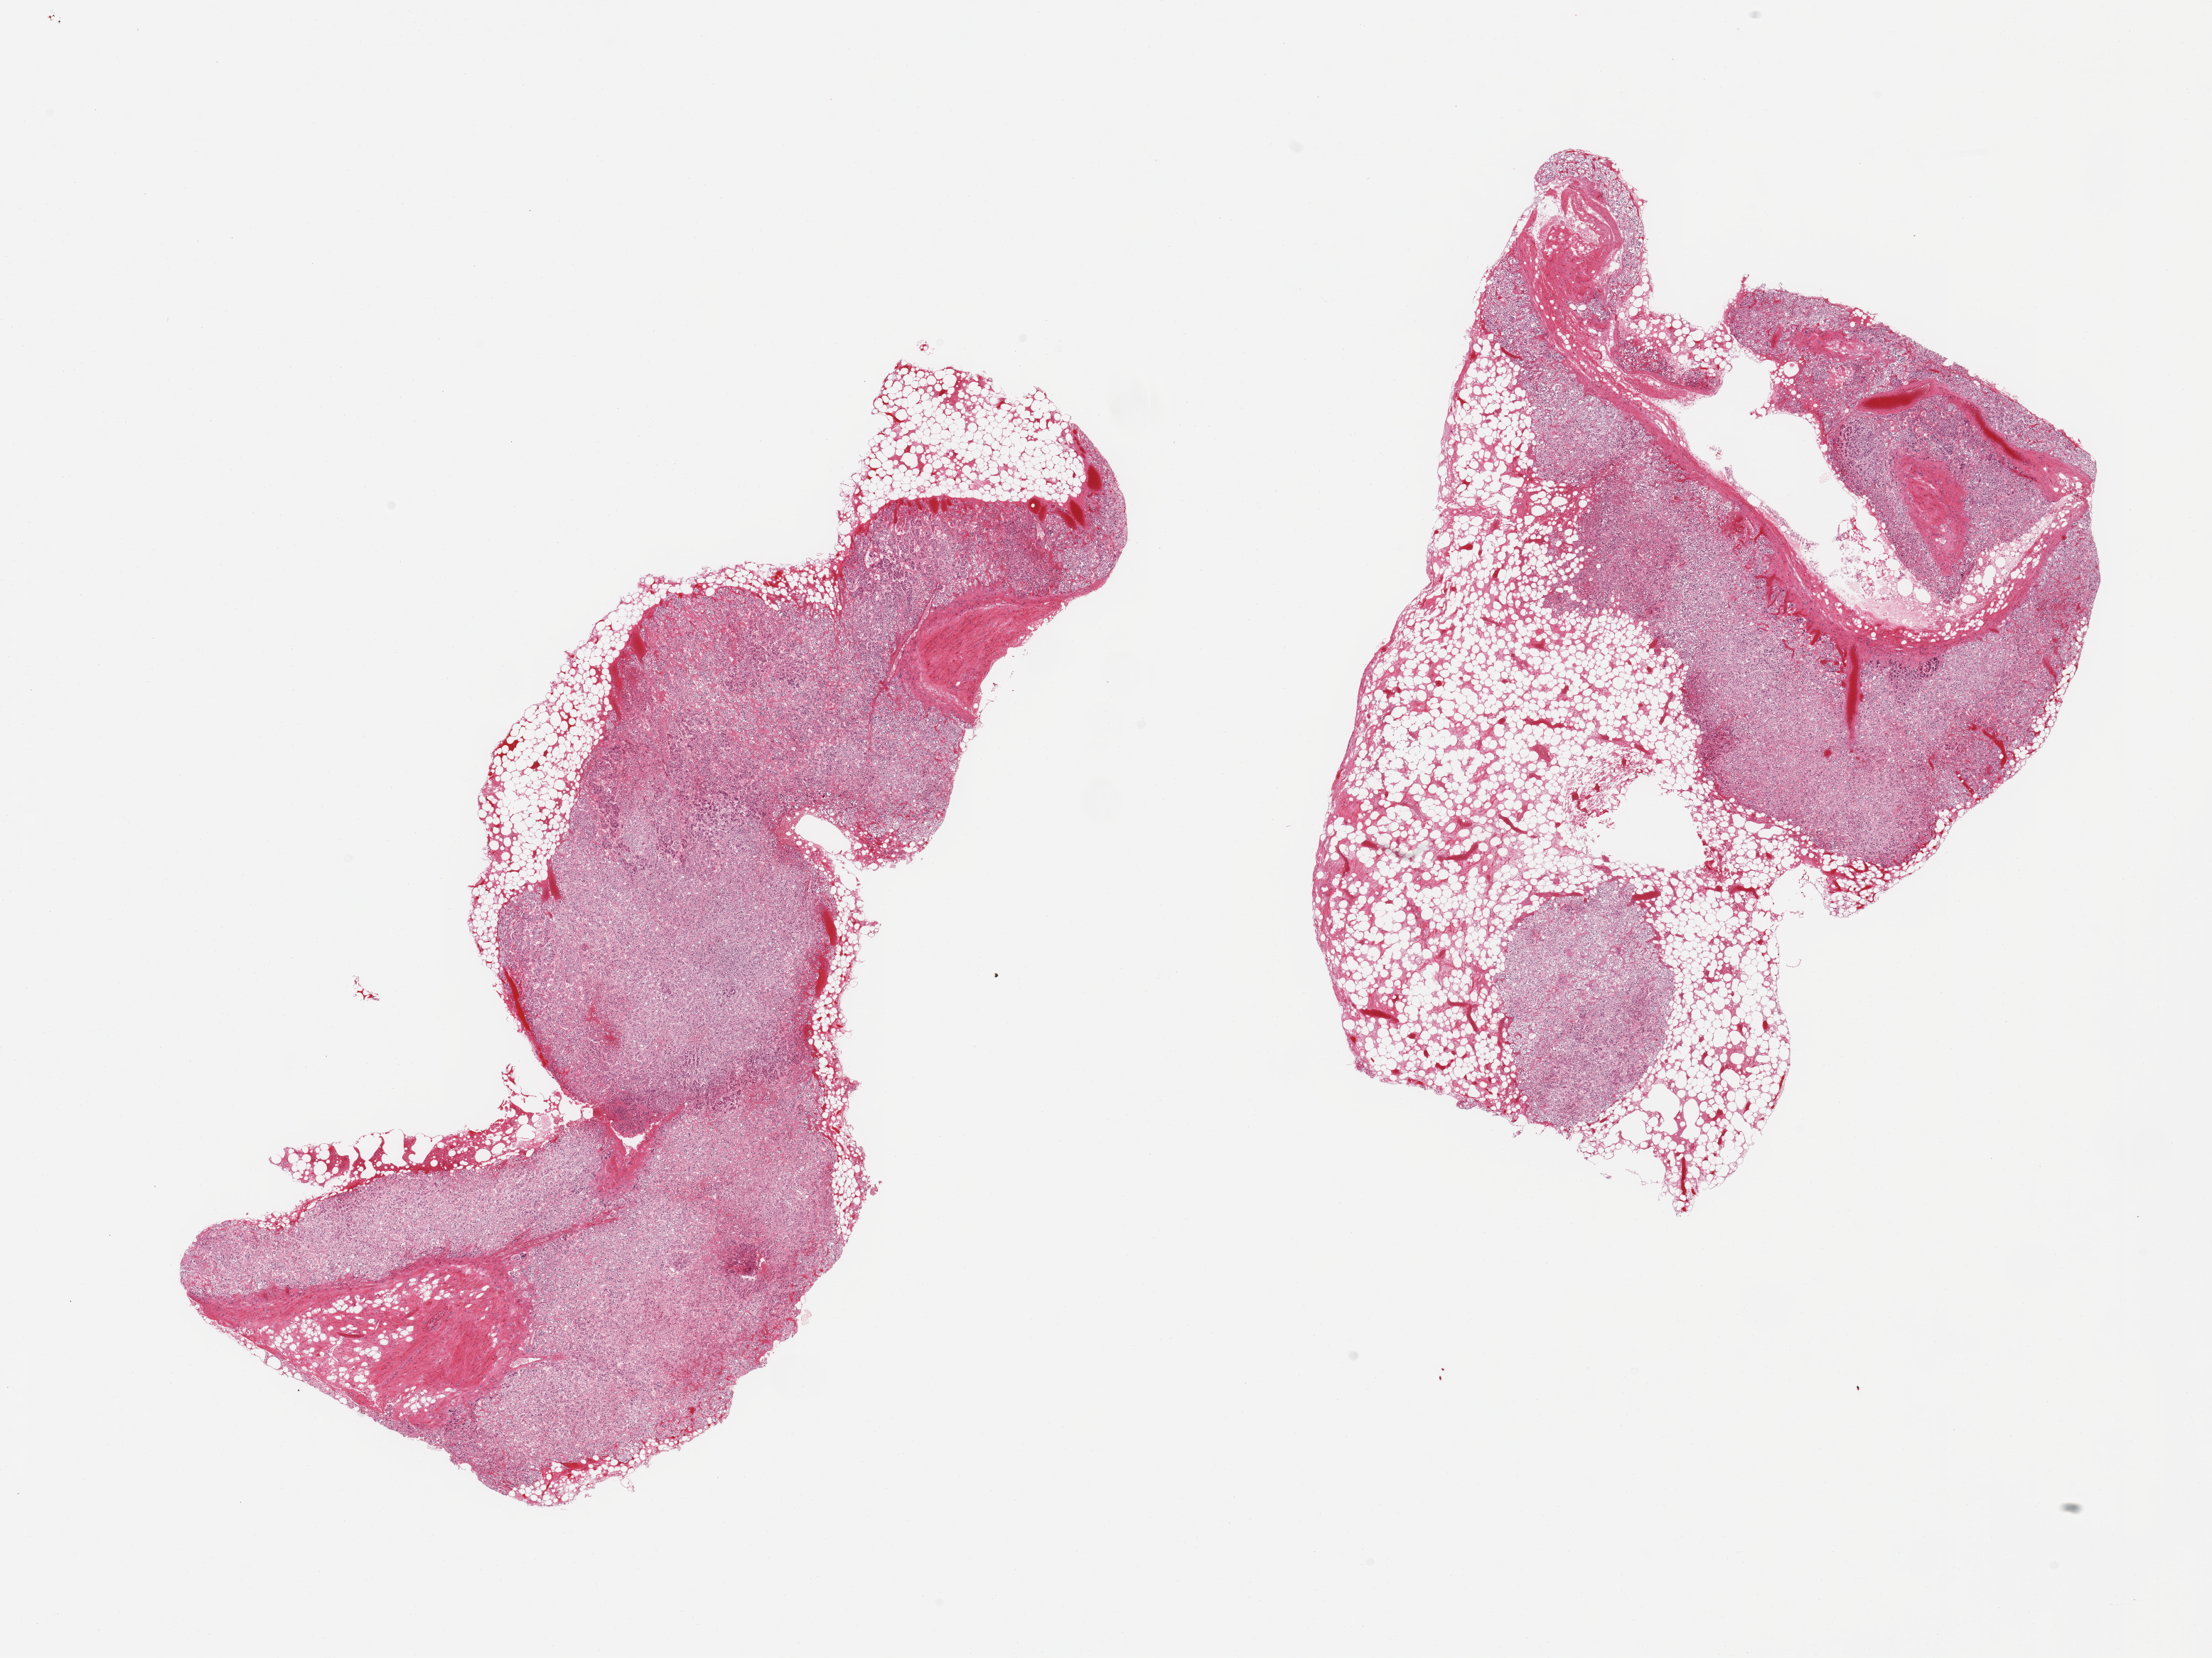
Digitized haematoxylin and eosin-stained section — low-resolution overview of the scanned area, about 24.6 x 18.4 mm (acquisition: 20x scan), PAXgene-fixed, paraffin-embedded tissue, section of adrenal gland (target tissue), donor tissue sample. Male donor.
Pathologist's review note for this sample: 2 pieces, advanced autolysis; ~30% adherent/interstitial fat.